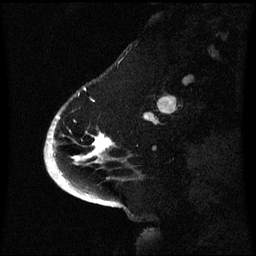
Breast MRI (dynamic contrast-enhanced), one sagittal slice; slice 17 of 60 in the series (ordered by position); dynamic contrast-enhanced series, image 2 of 3 at this slice position (ordered by acquisition); 1.5 T; TE 4.2 ms, TR 8.4 ms; 256 × 256 image matrix, field of view 220 × 220 mm. Female patient, age 53 years. Case-level facts recorded for this patient, not image findings: setting: breast cancer imaged before/during neoadjuvant chemotherapy; receptor status: HR-positive, HER2-negative.
Annotated regions visible in this slice (semi-automatically segmented with operator editing):
- analysis volume of interest (the breast-tissue region the enhancement analysis was run in; not a lesion): box from (x=52, y=106) to (x=128, y=171) px
- tumour enhancement mask (voxels above the 70 % enhancement threshold inside the analysis volume of interest): (x=52, y=116)–(x=114, y=167)